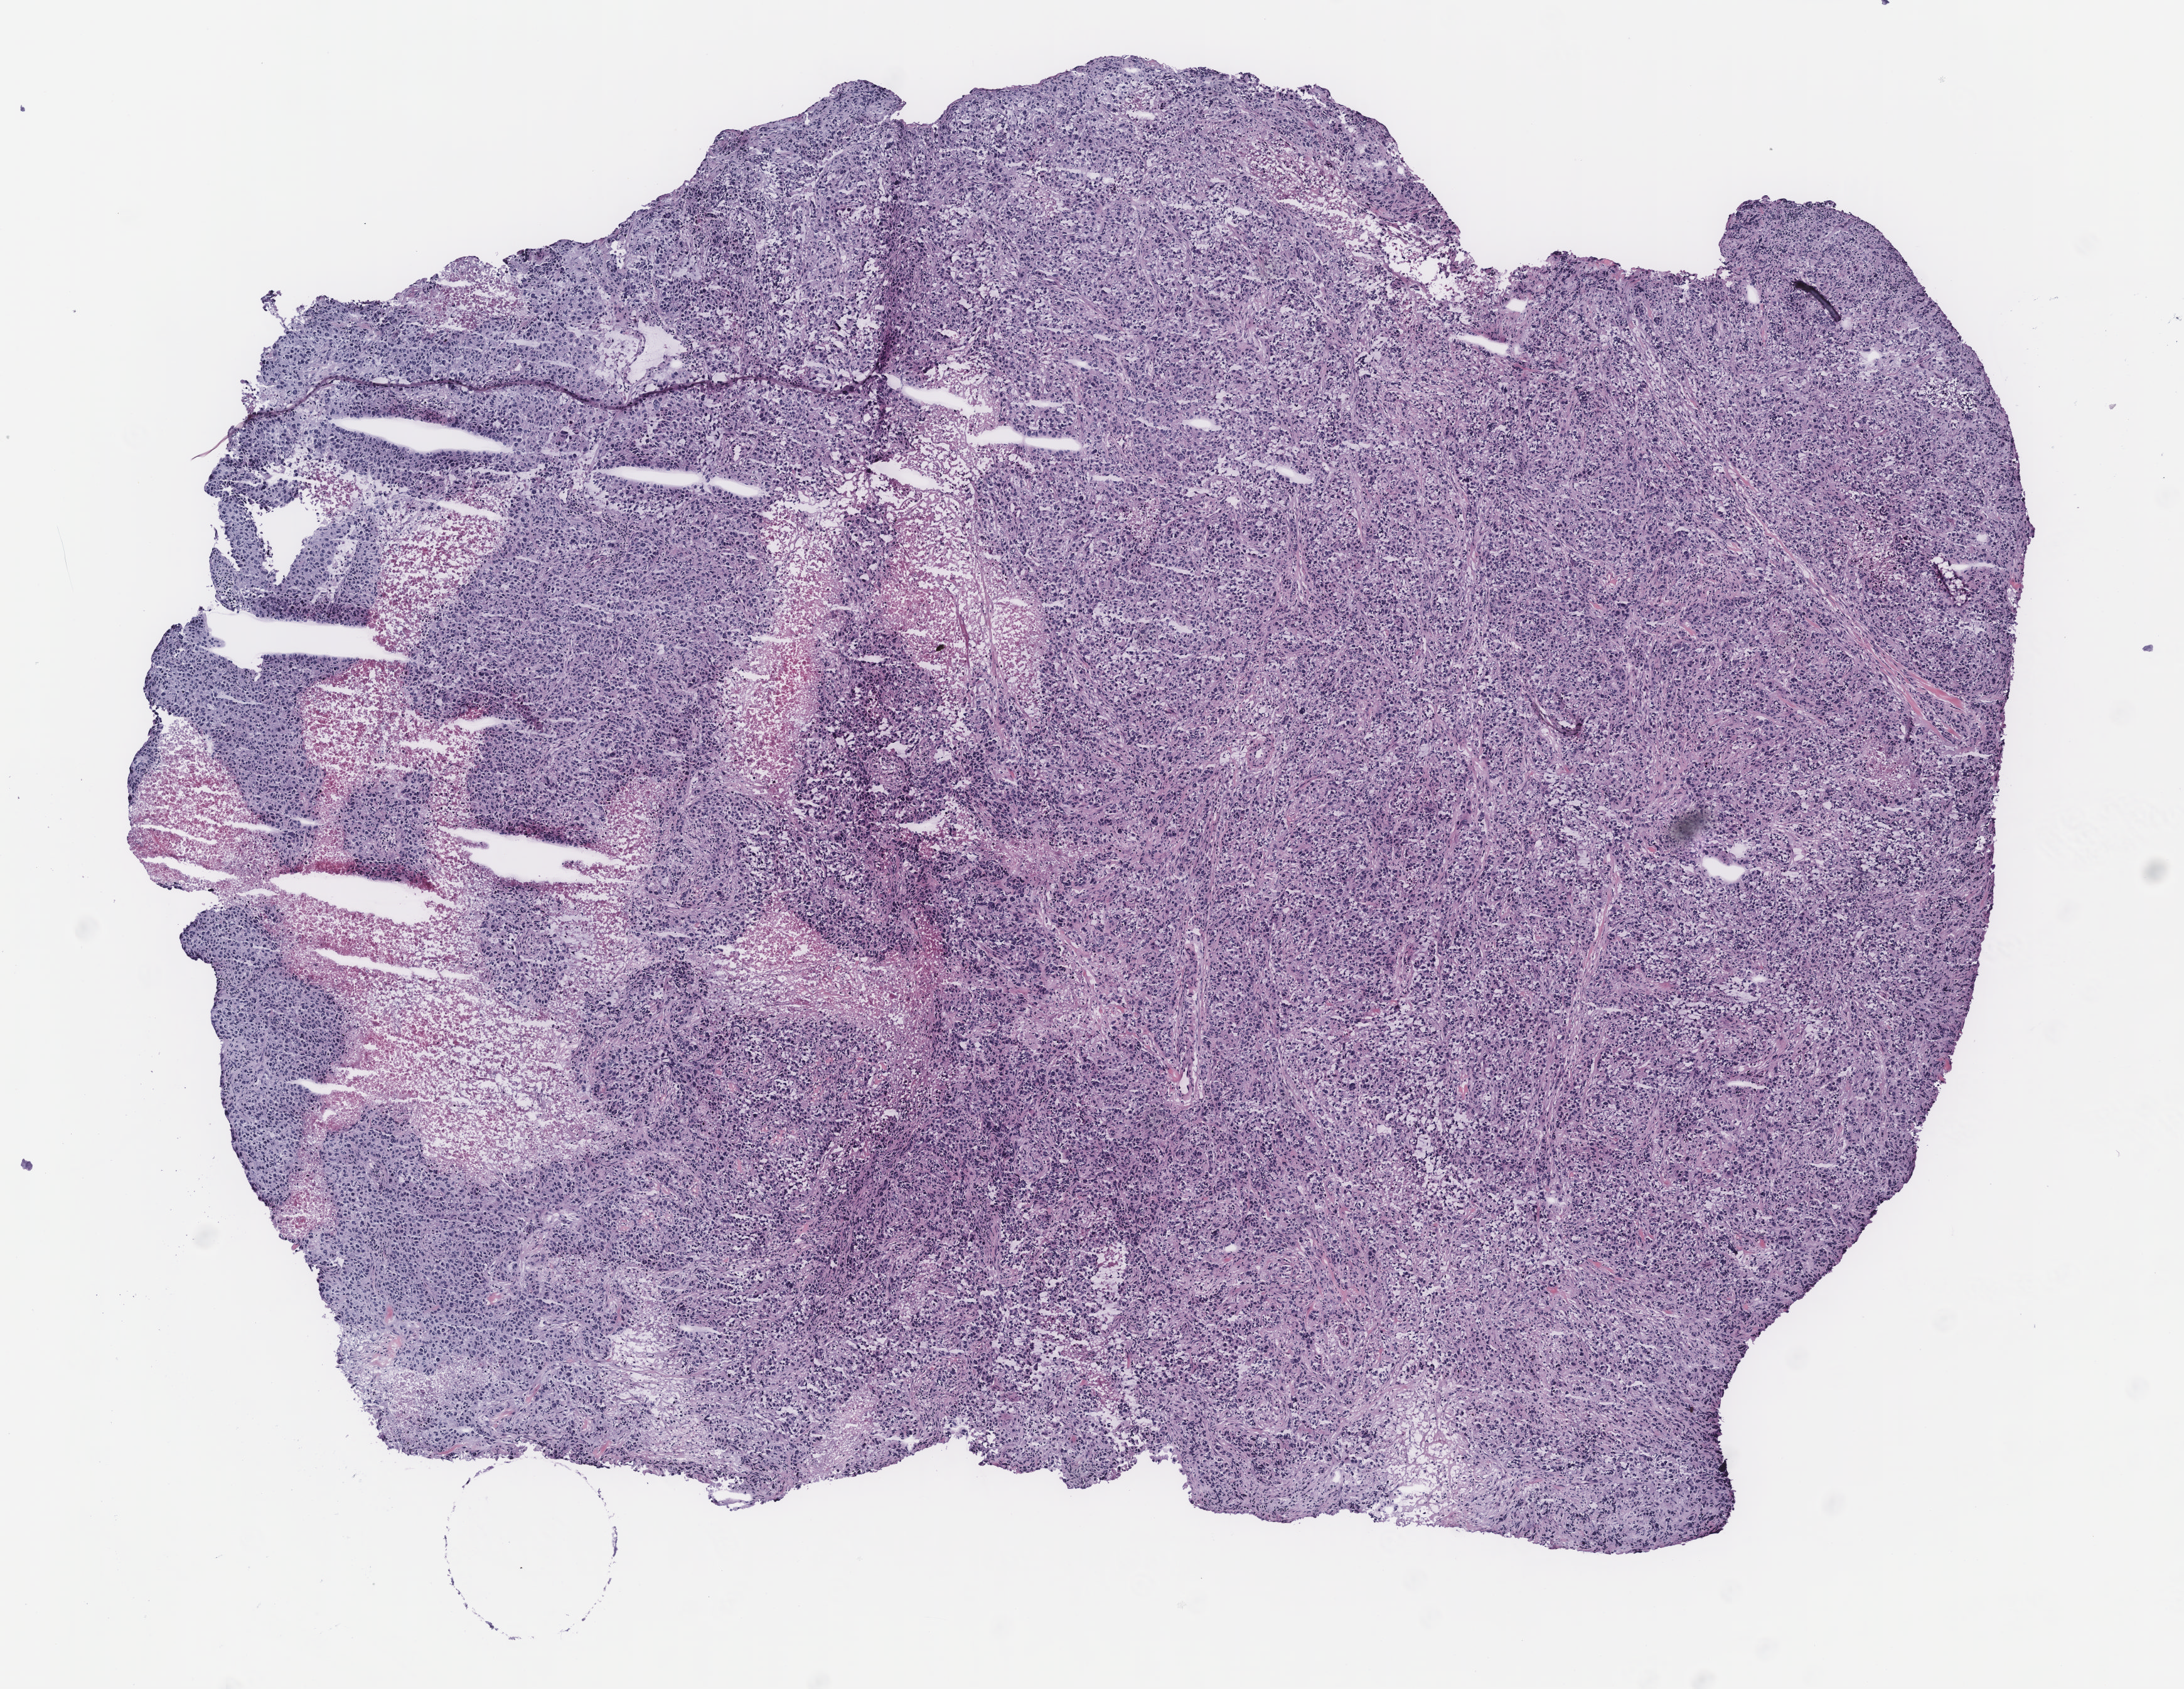
H&E whole-slide image — shown as a low-resolution overview of the whole scanned area (about 7.0 x 5.4 mm, acquisition: 40x scan), tumour tissue sample, breast. Female, 42 y/o.
- histologic diagnosis: Infiltrating duct carcinoma, NOS
- AJCC pathologic stage: IIA